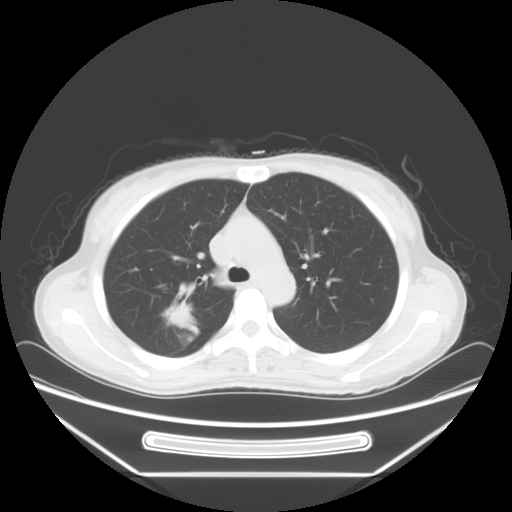
Chest CT, one axial slice; slice 47 of 66 in the series (ordered by position); 120 kVp; lung window (W 1500 / L -600 HU); 5 mm slice thickness; 512 × 512 image matrix, field of view 408 × 408 mm. Female patient, age 37 years. From the clinical record (not read from this slice): clinical TNM (as recorded): T1c N0 M1.
Outlined on this slice (rectangle marked by the reading radiologist):
- lung tumour (recorded histology: adenocarcinoma): bounding box <166,295,195,331> (left, top, right, bottom; pixels)